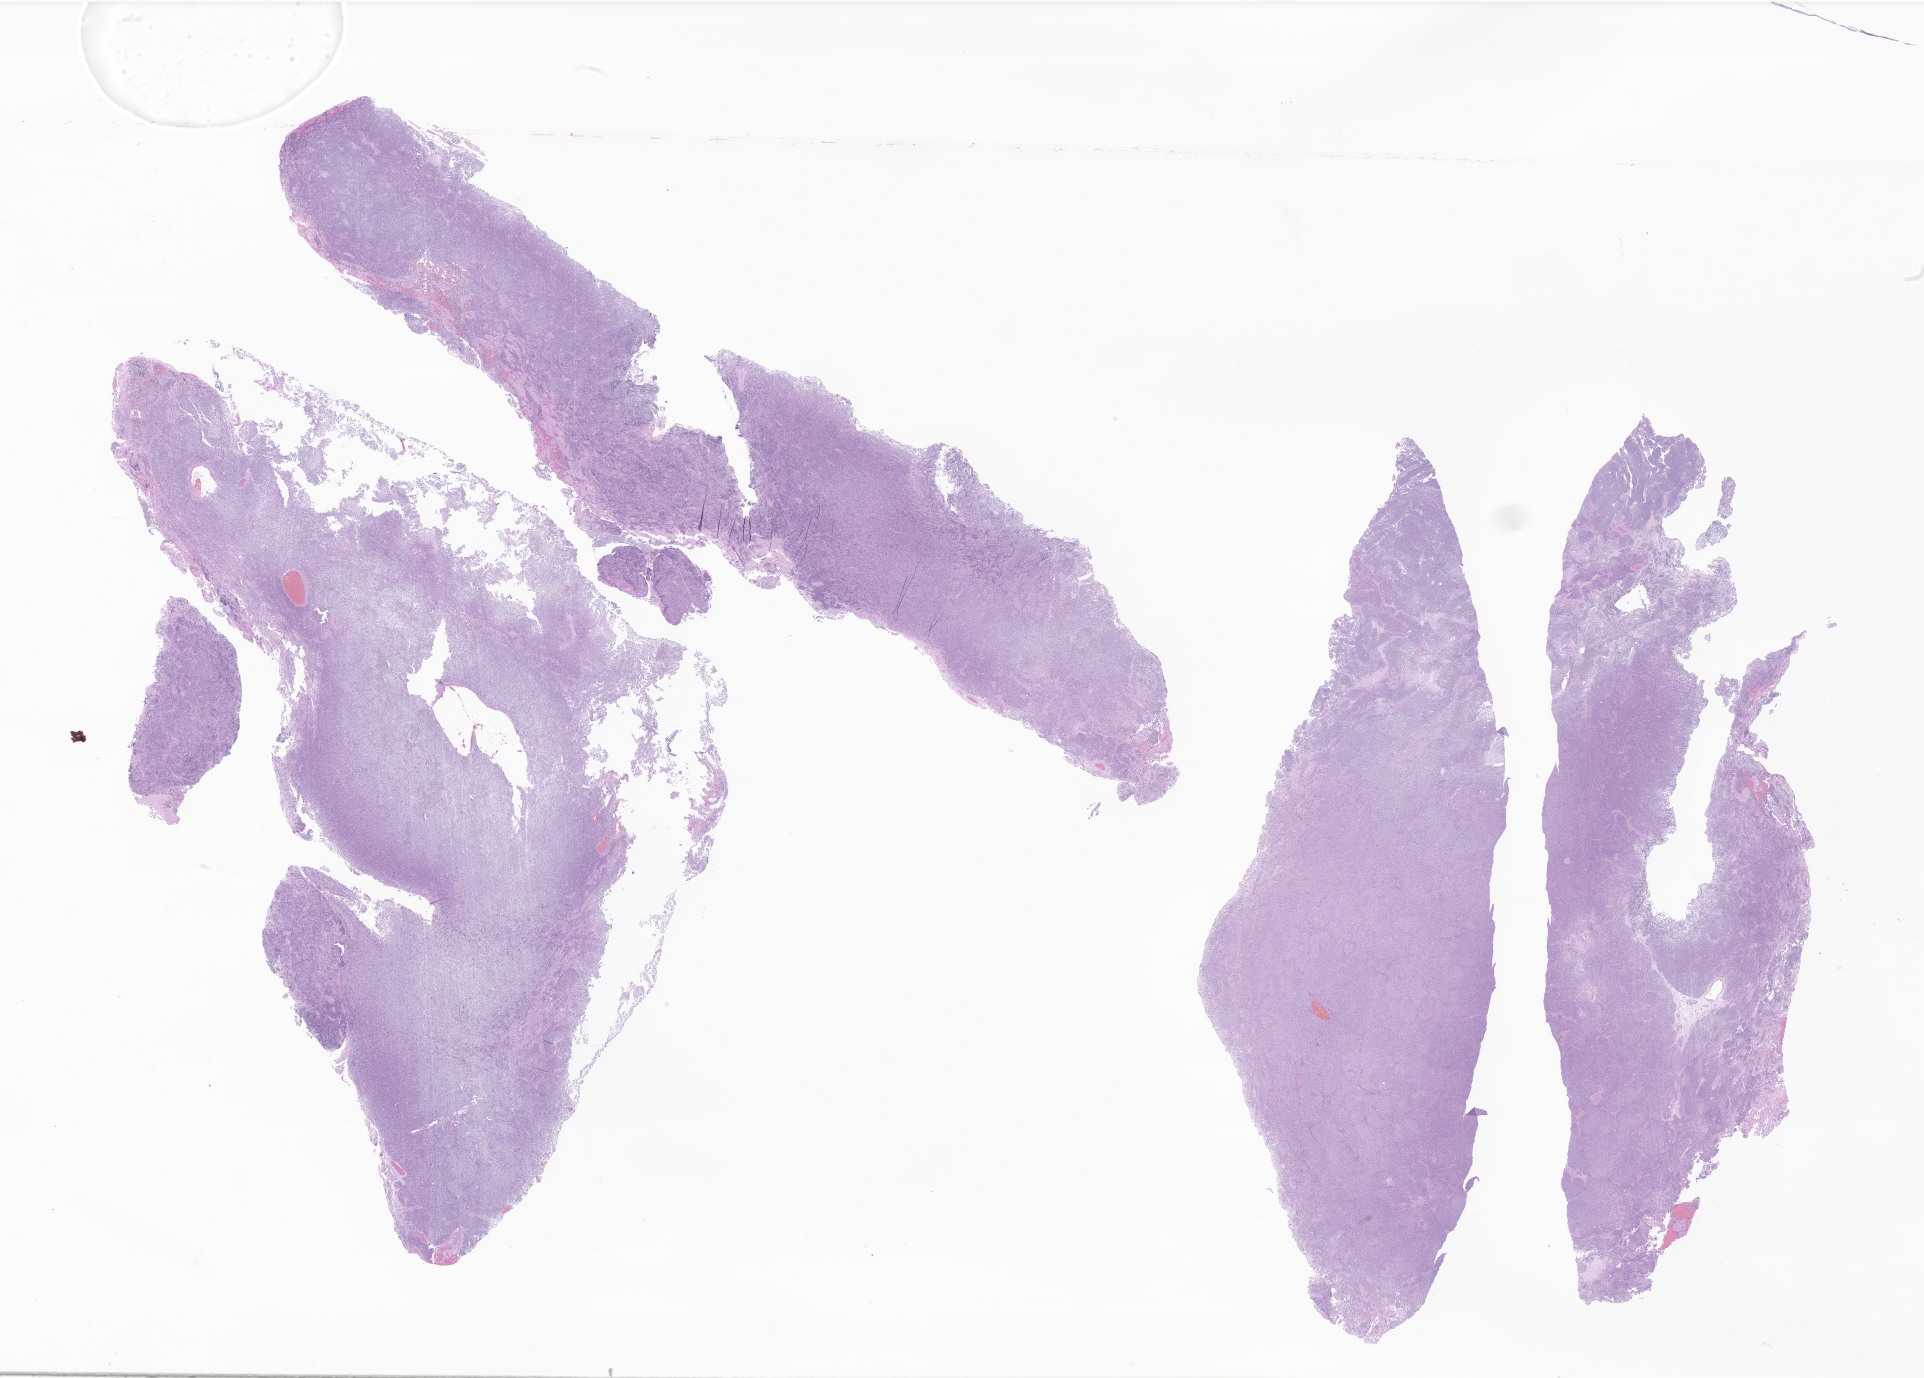
Hematoxylin and eosin (H&E) whole-slide image of tumor tissue from the cerebellum, whole scanned area (about 32.4 x 23.2 mm) shown as a low-resolution overview; formalin-fixed, paraffin-embedded (FFPE) tissue. Patient male; age 110 months (9 years 2 months).
- recorded diagnosis: Medulloblastoma, NOS